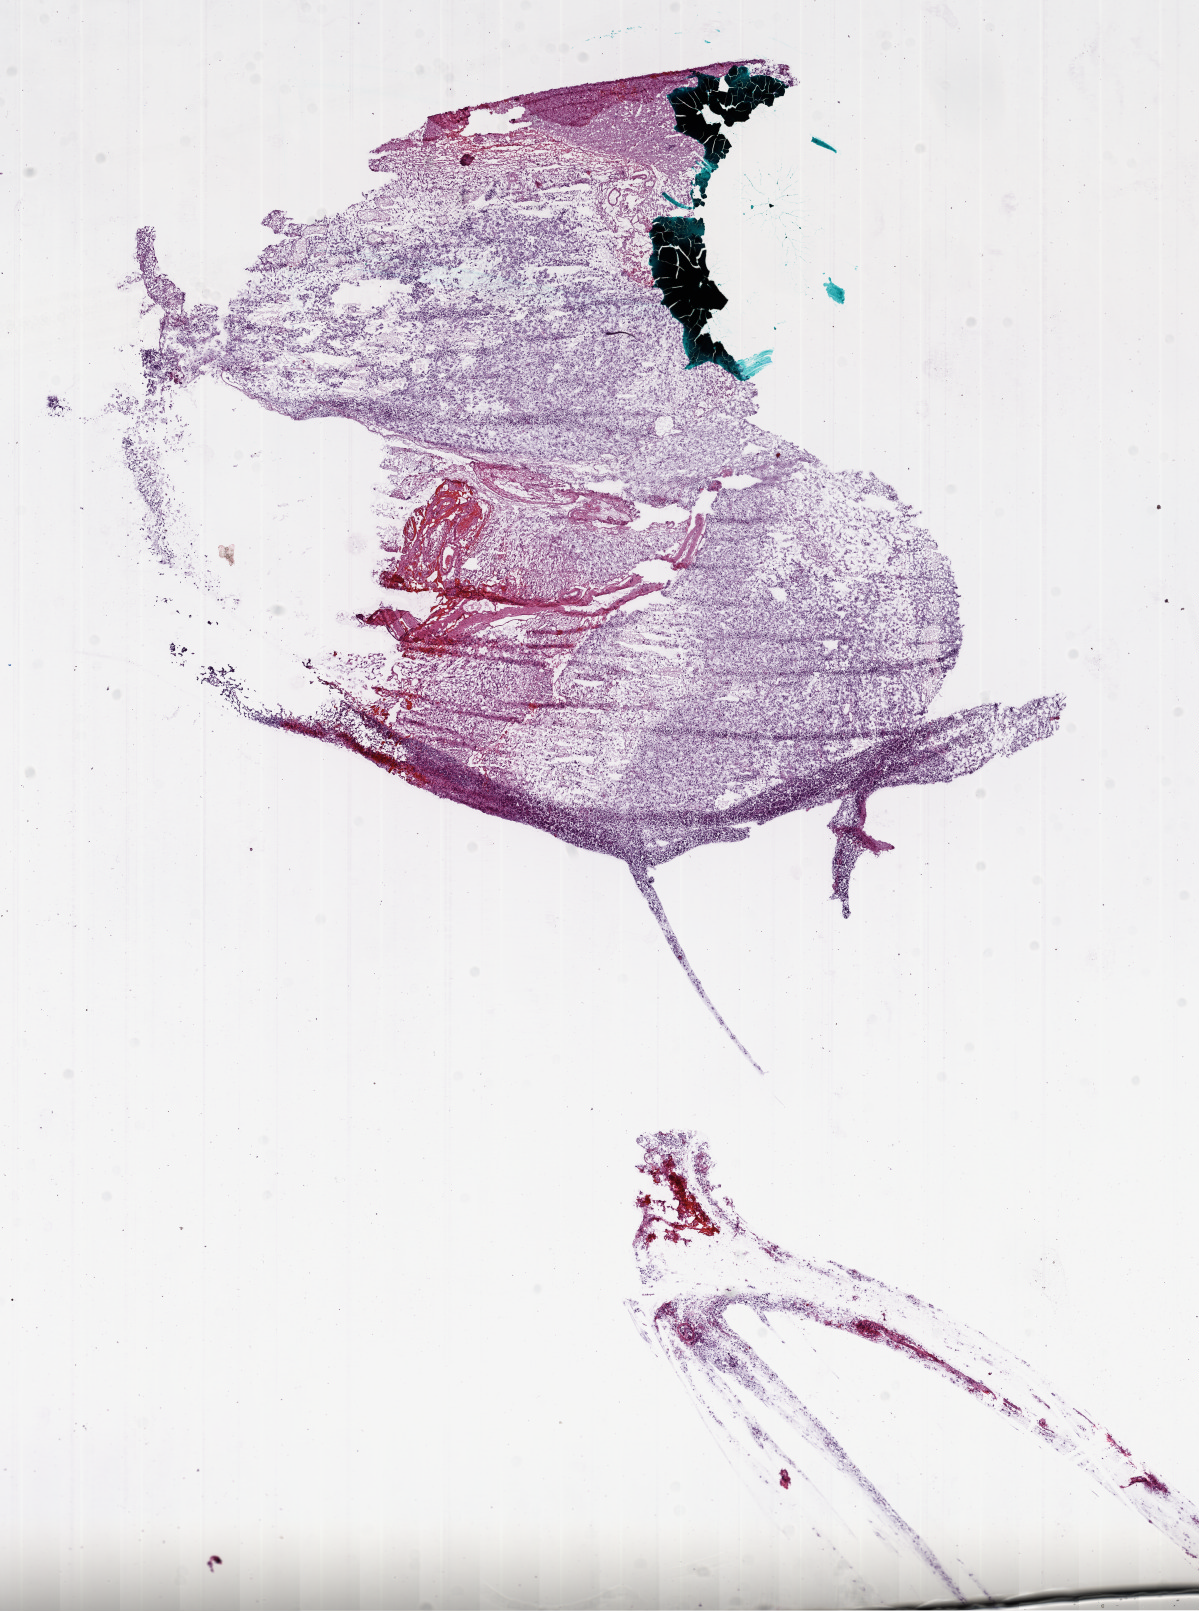
H&E-stained whole-slide image — low-resolution overview of the scanned area, about 9.7 x 13.0 mm (from a 20x scan); frozen section from the bottom of the tissue portion; primary tumour sample from the brain. Female, age 17 years at initial diagnosis. Slide review estimates, as recorded: tumour cells 80%, tumour nuclei 90%, normal cells 0%, stromal cells 10%, necrosis 10%.
Pathologic diagnosis: Glioblastoma.